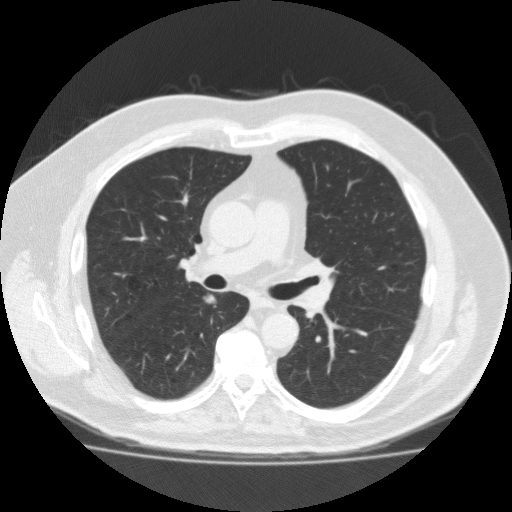
Low-dose screening chest CT, axial slice. Third annual screen. Lung window (W 1500 / L -600 HU). 2 mm slice thickness. Standard (soft-tissue) reconstruction kernel (FC10). 120 kVp. 512 × 512 image matrix, field of view 391 × 391 mm. Male, age 56 years at enrolment.
Expert reader's lesion annotation, bounding box <186,281,233,319> (left, top, right, bottom; pixels). Reader record for this screening exam (exam-level; its link to the box is not recorded): non-calcified nodule or mass ≥4 mm, right lower lobe, 12 × 8 mm, spiculated (stellate) margins, soft tissue attenuation, pre-existing on the prior screen: yes; interval growth: yes. Official screen result: positive, other.